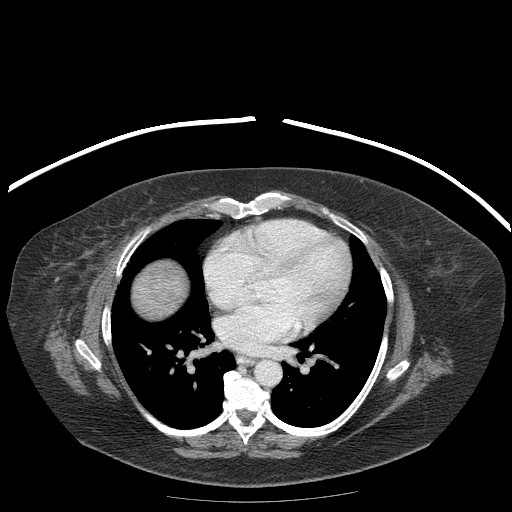
Contrast-enhanced abdominal CT (liver protocol), one axial slice; position 189 of 204 along the scan axis; reconstruction kernel STANDARD; 120 kVp; soft-tissue window (W 400 / L 40 HU); 2.5 mm slice thickness; 512 × 512 image matrix. Case-level facts recorded for this patient, not image findings: diagnosis: hepatocellular carcinoma (patient treated with transarterial chemoembolisation; whether this scan precedes or follows treatment is not stated here); TNM stage (as recorded): Stage-IIIB; Child-Pugh class: A; tumour differentiation: well differentiated; tumour nodularity: uninodular.
Annotated regions visible in this slice (semi-automatically segmented with operator editing):
- liver parenchyma outside the tumour (the mass and vessels are separate outlines, so this box may not span the whole liver): bounding box (x1, y1, x2, y2) in pixels: (132, 260, 185, 316)